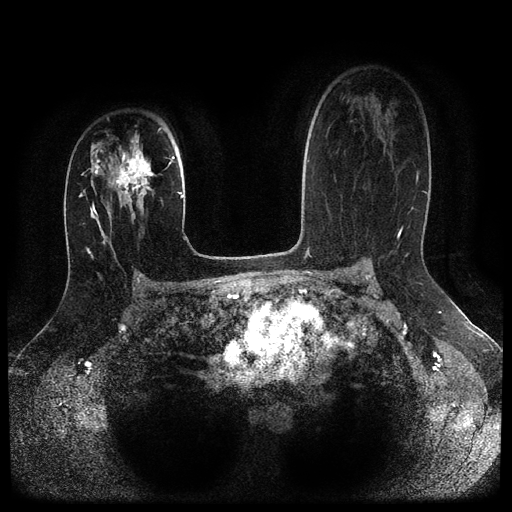
Breast MRI (dynamic contrast-enhanced, multi-phase), one axial slice. Slice 66 of 116 in the series (ordered by position). Dynamic contrast-enhanced series, time point 2 of 5 at this slice position (early post-contrast). 1.5 T. TE 2.6 ms, TR 5.4 ms. 2 mm slice thickness. 512 × 512 image matrix, field of view 340 × 340 mm. Female patient, age 29 years.
Annotated regions visible in this slice (semi-automatically segmented with operator editing):
- breast lesion (labelled 'tumour' in the annotation; benign lesions carry a separate 'benign' label): box from (x=110, y=135) to (x=160, y=217) px